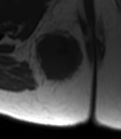
MRI of an extremity soft-tissue mass, one axial slice. Position 25 of 47 along the scan axis. MR volume resampled by the dataset authors to the PET/CT grid (not the native acquisition matrix). 3.27 mm slice thickness. 121 × 139 image matrix, field of view 118 × 136 mm. Female patient. From the clinical record (not read from this slice): histological type: epithelioid sarcoma; grade: intermediate; site of the primary tumour: right buttock.
Structures marked on this image (expert contour drawn on MRI and transferred to this co-registered scan by the dataset authors):
- gross tumour volume including surrounding oedema: bounding box [x1, y1, x2, y2] px = [29, 27, 83, 87]
- gross tumour volume (mass): [34, 32, 83, 81]